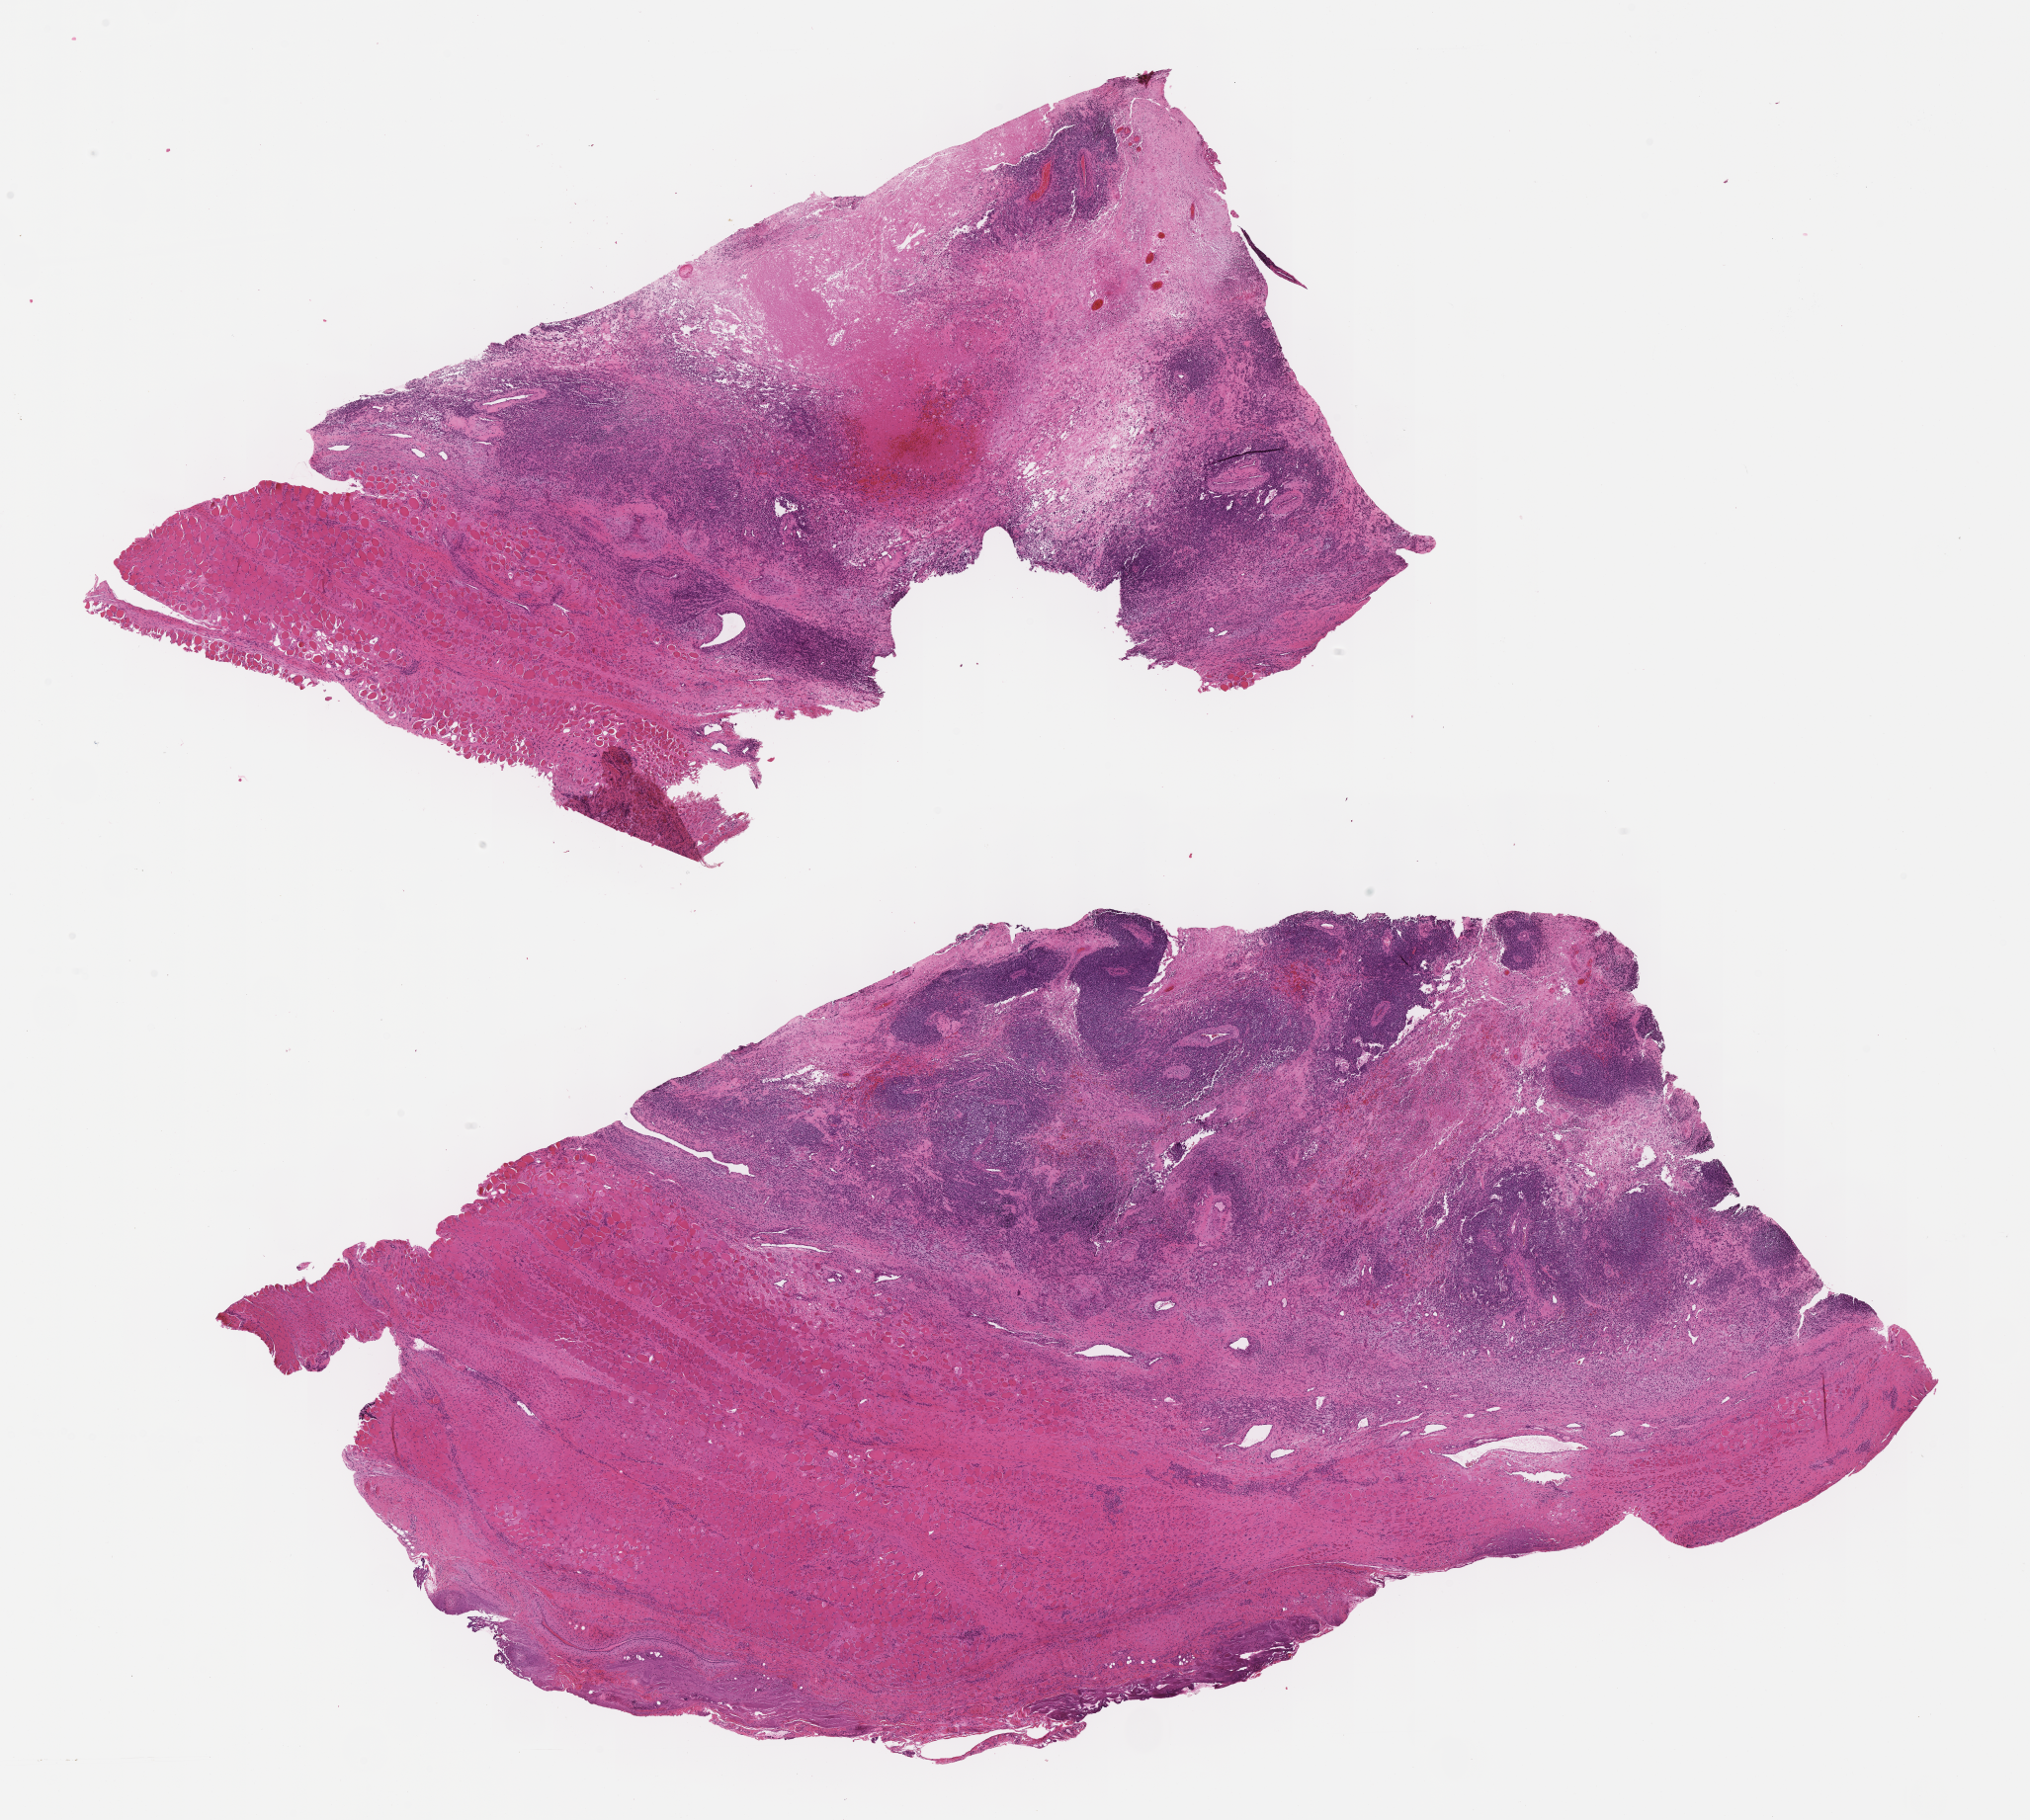
Hematoxylin and eosin (H&E) whole-slide image of tumor tissue, low-resolution overview of the scanned area, about 16.6 x 14.9 mm. Formalin-fixed, paraffin-embedded (FFPE) tissue. Sample anatomic site: soft tissue, calf-right. Male patient, age at diagnosis 4.6 years.
- diagnosis: rhabdomyosarcoma; histological classification: alveolar rhabdomyosarcoma
- primary site (case record): leg
- metastatic status at presentation (as recorded): metastatic (confirmed)
- stage (as recorded): 4